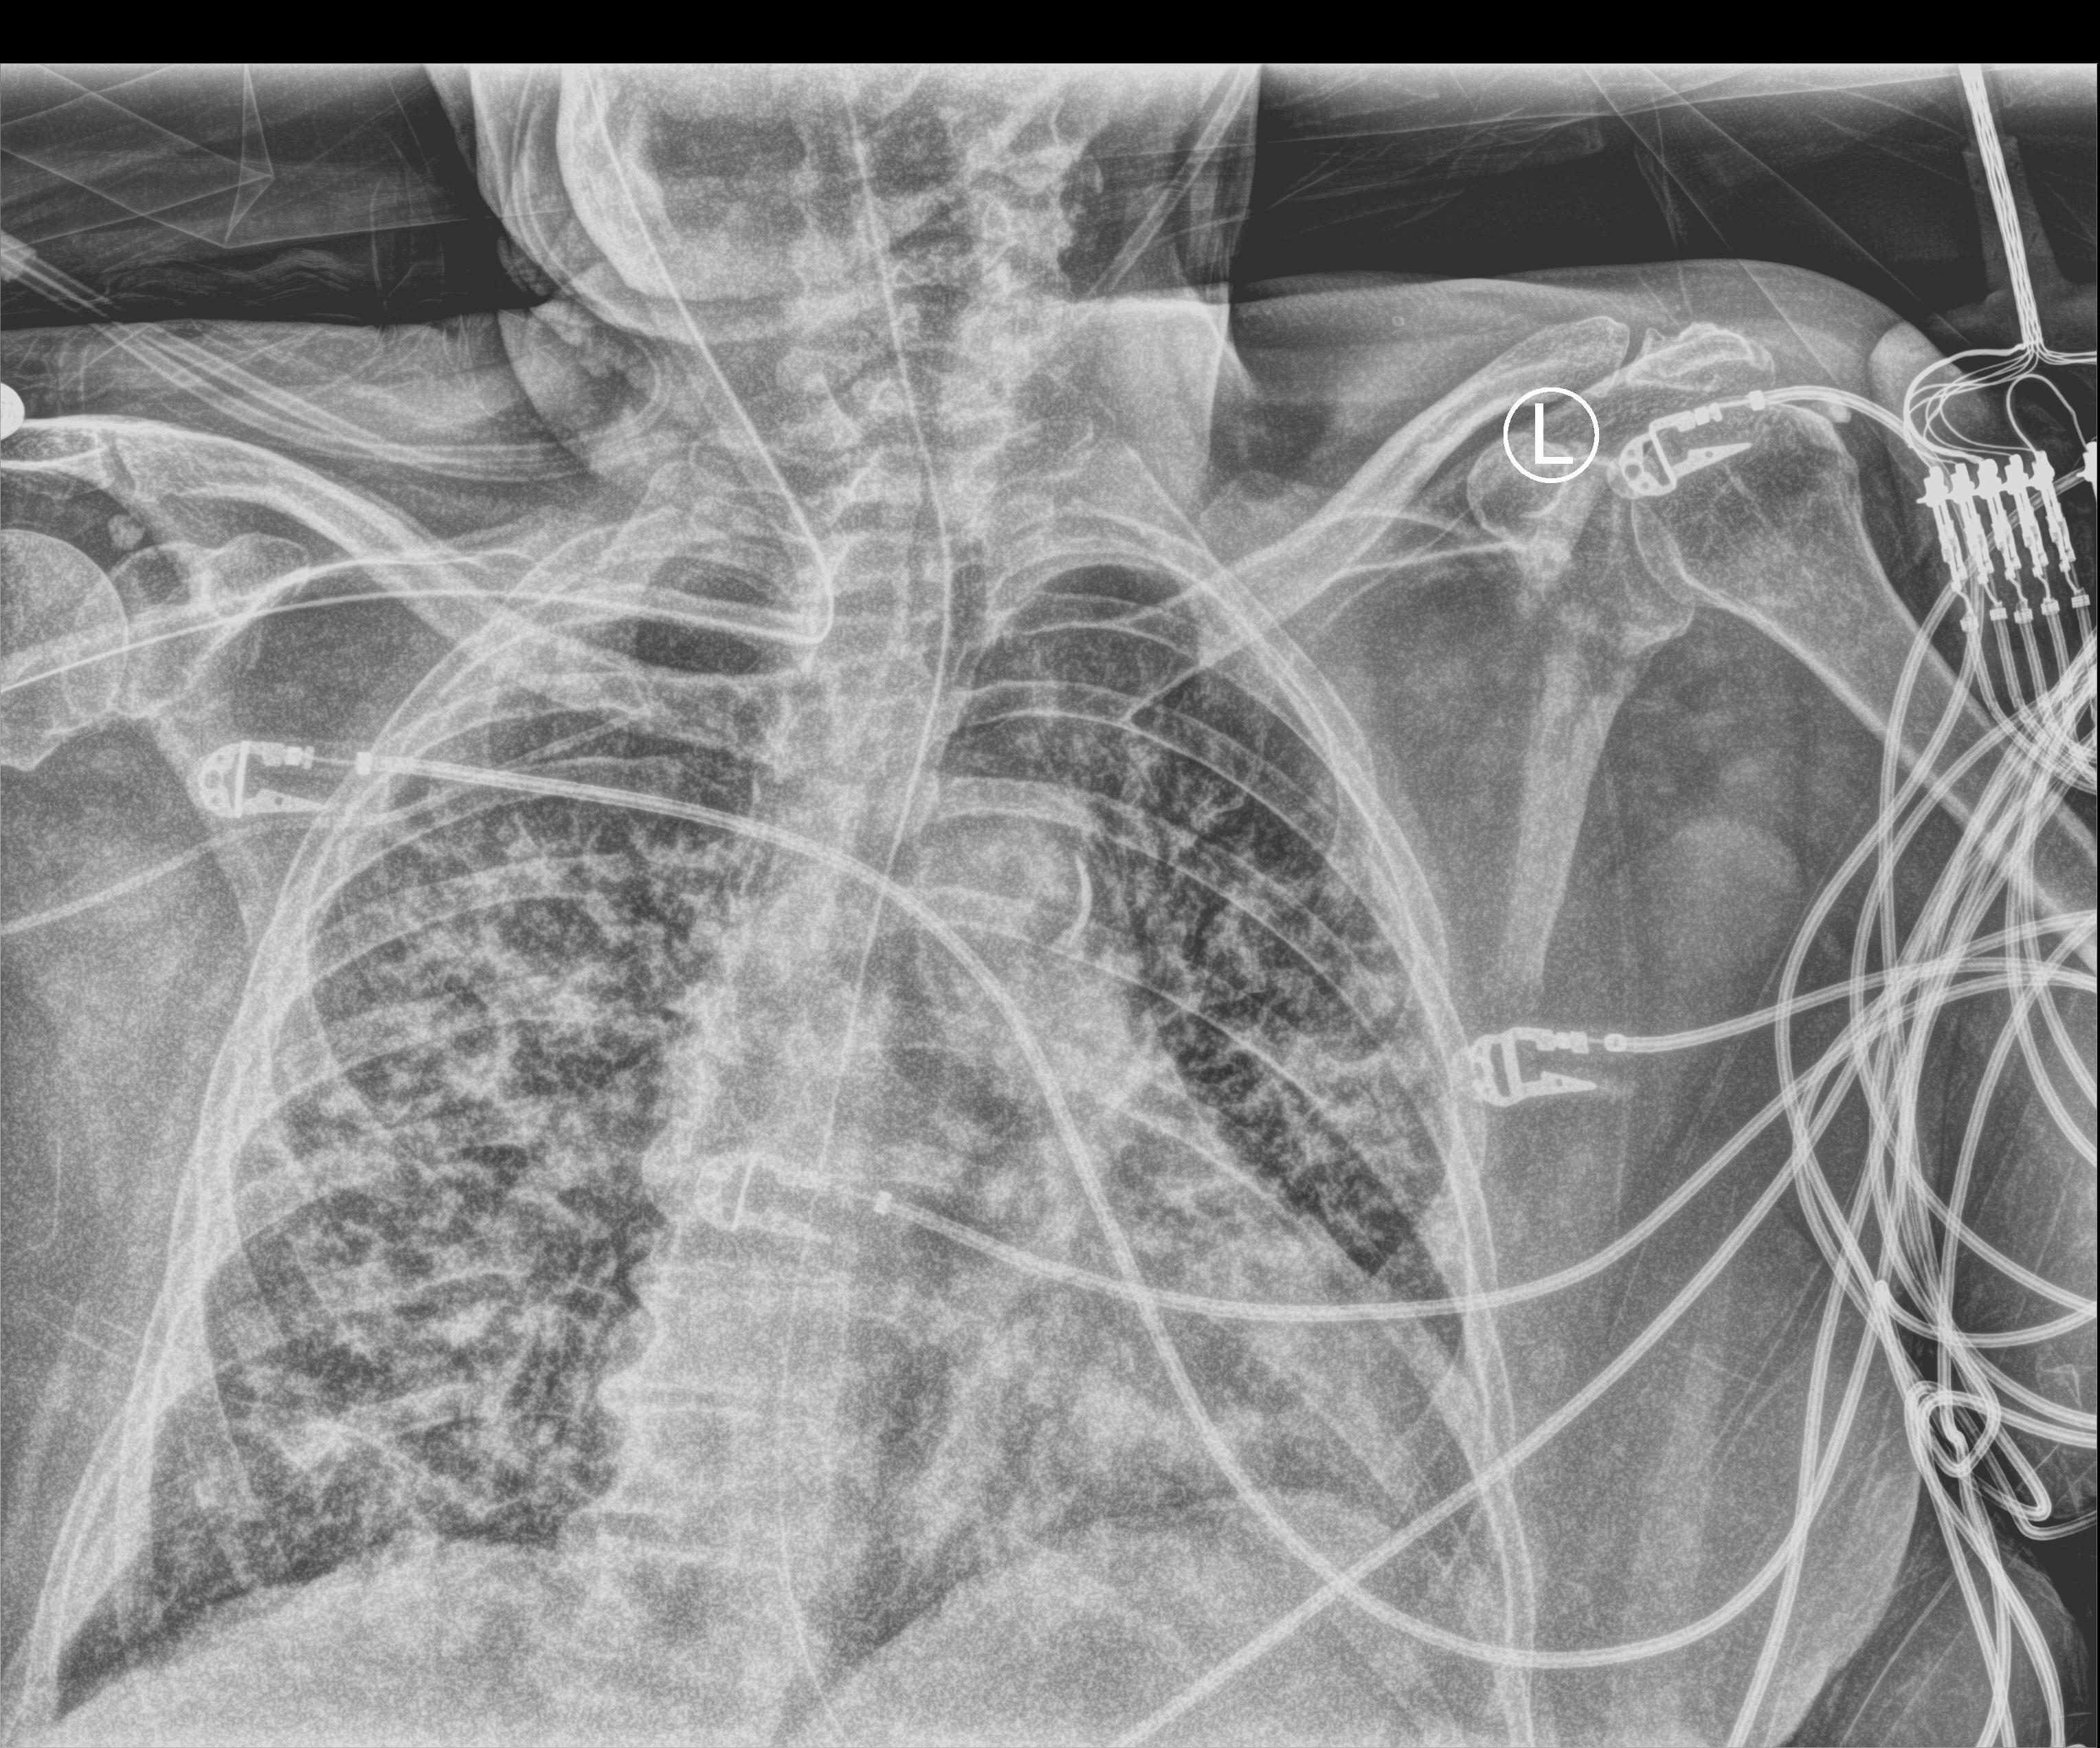
Portable chest radiograph, anteroposterior (AP) projection. Patient hospitalised with COVID-19; female, aged 75–90 years.
From the hospital-stay record, not from the radiograph (when in the stay this image was taken is not recorded): mechanically ventilated during this hospital stay: yes.